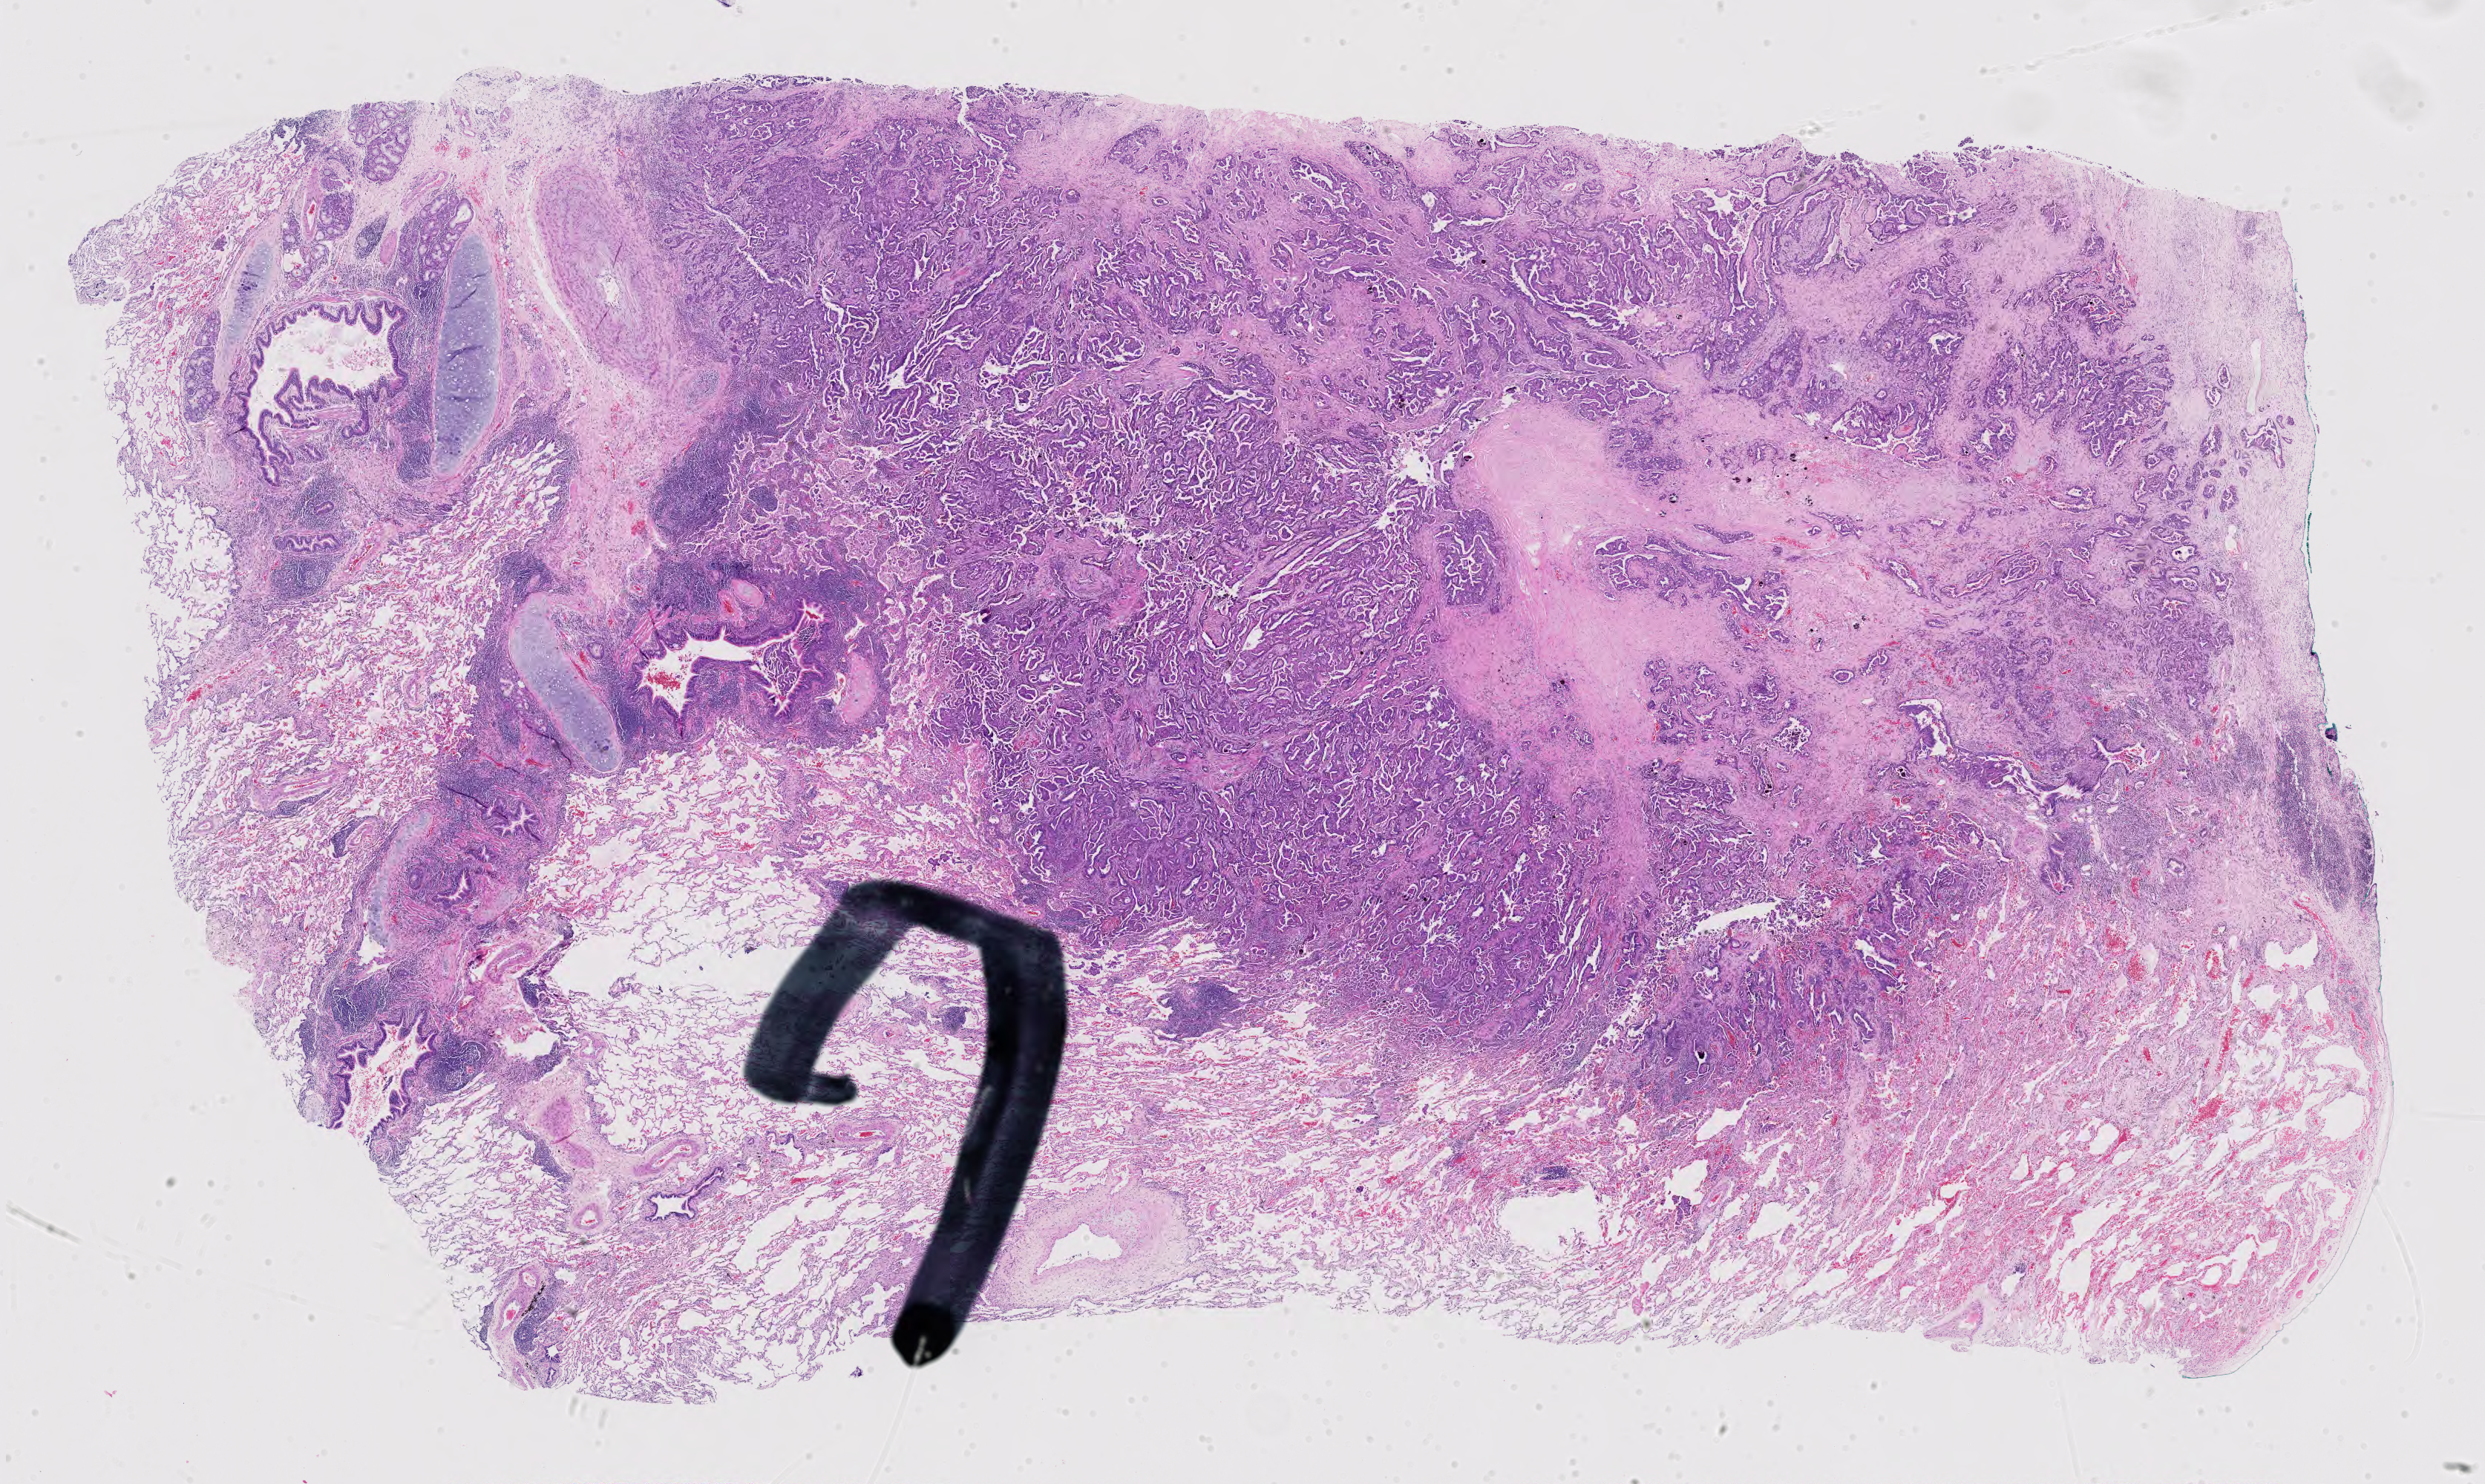
Digitized Hematoxylin and eosin (H&E) stained tissue section (whole slide), low-resolution overview of the scanned area, about 24.3 x 14.5 mm. FFPE section. Sample: primary tumour, lung. Female patient; age at initial diagnosis 42 years.
AJCC pathologic stage: IB (7th edition). Histologic diagnosis: Adenocarcinoma with mixed subtypes. TNM: T2a N0 M0. Laterality: right.